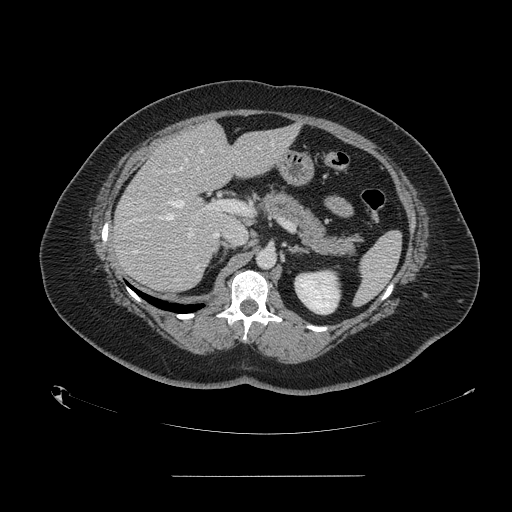
Contrast-enhanced abdominal CT, one axial slice. Position 89 of 164 along the scan axis. 120 kVp. Intravenous contrast given. Soft-tissue window (W 400 / L 40 HU). 2.5 mm slice thickness. 512 × 512 image matrix, field of view 495 × 495 mm. Female patient, age 52 years. From the clinical record (not read from this slice): diagnosis: colorectal cancer liver metastases, imaged before liver resection; multiple liver metastases: yes; largest metastasis: 3.5 cm; disease in both lobes: no.
Outlined on this slice (outlined manually by an expert reader):
- hepatic veins: bounding box (x1, y1, x2, y2) in pixels: (166, 144, 273, 220)
- liver: (114, 123, 296, 291)
- planned liver remnant (the part of the liver to remain after resection): (177, 123, 296, 224)
- portal vein (with intrahepatic branches): (174, 189, 245, 237)